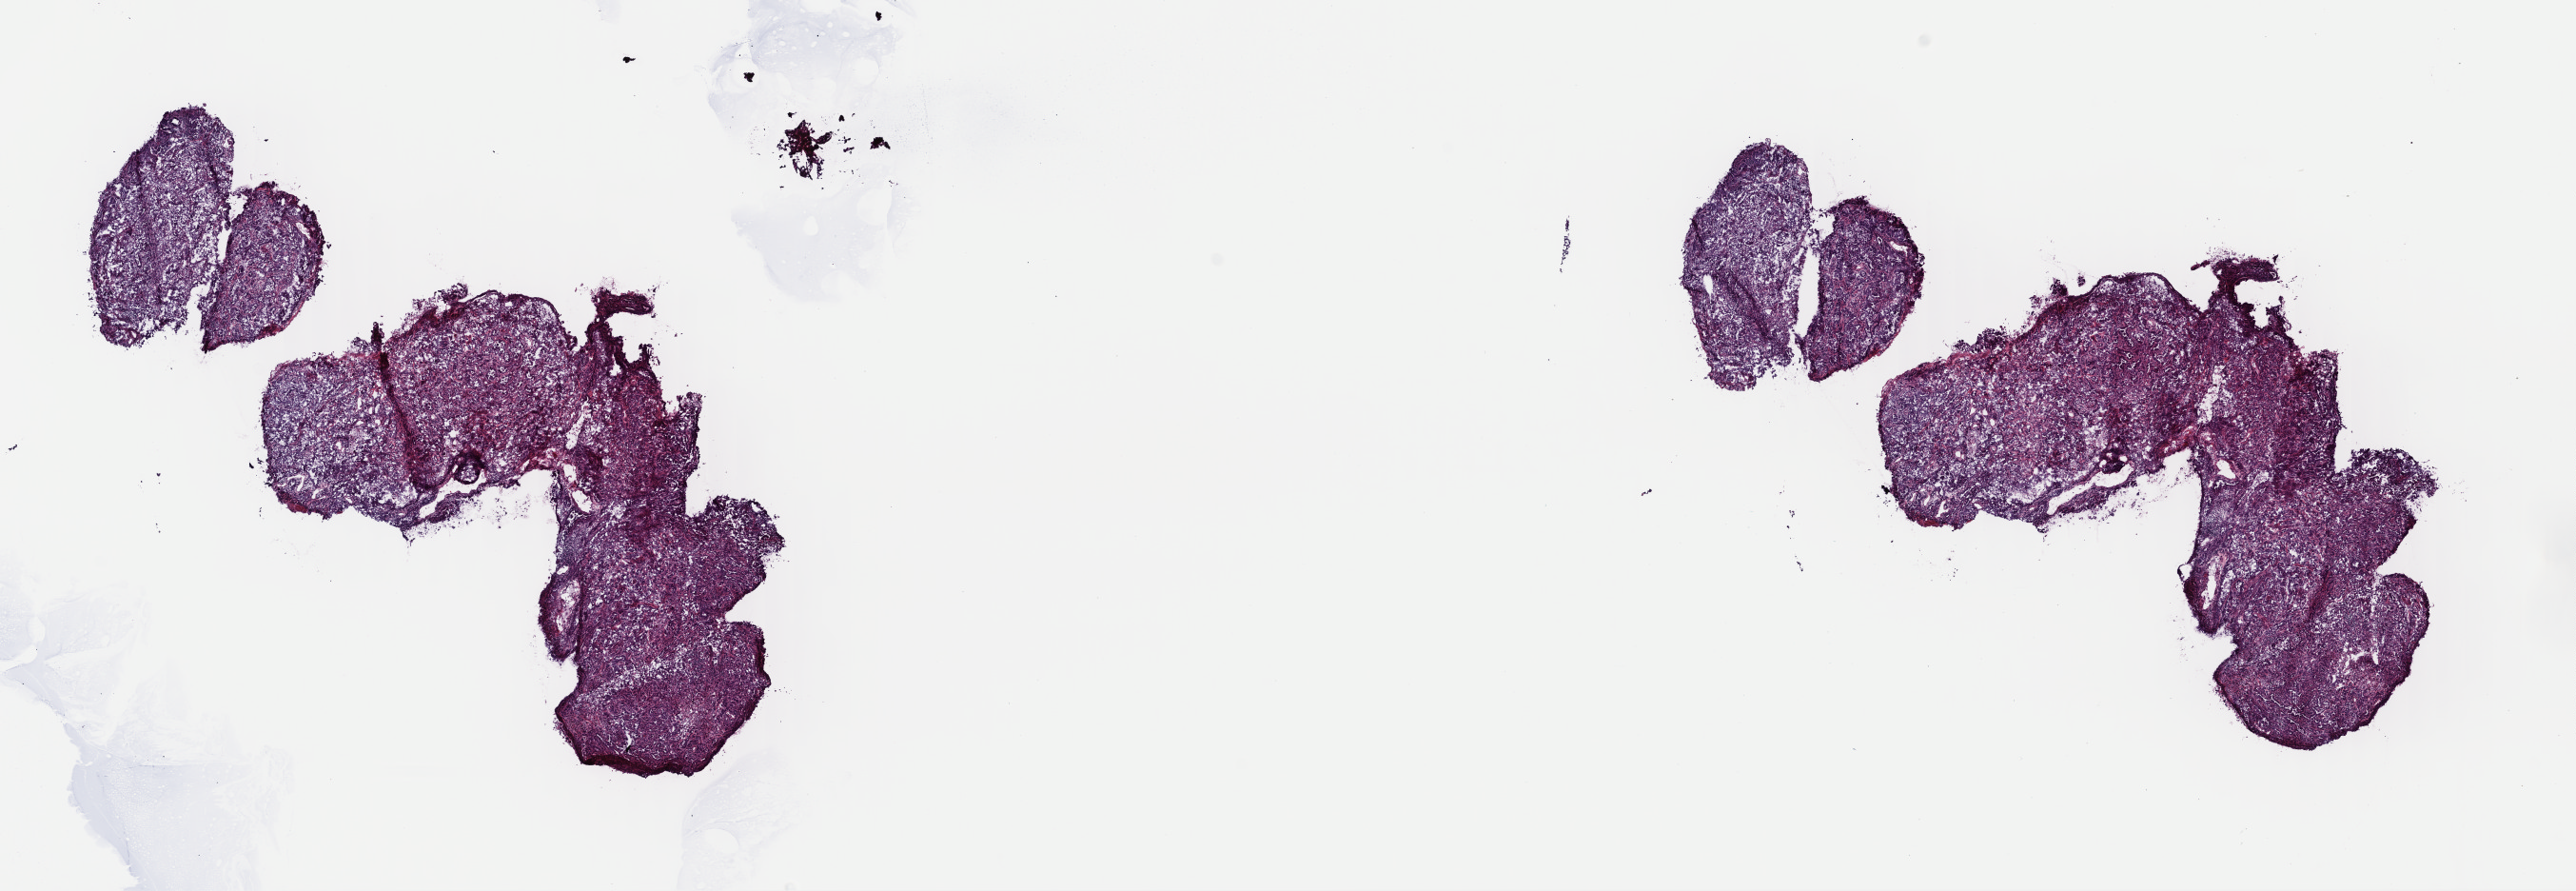
H&E whole-slide image, a low-resolution overview of the entire scanned area, about 21.3 x 7.4 mm. Frozen section from the top of the tissue portion. Sample: primary tumour, uterus. Female patient; age at initial diagnosis 56 years. Histologic grade: G3 (poorly differentiated). Pathologist review of this section (percent, as recorded): tumour cells 97%, tumour nuclei 80%, normal cells 0%, stromal cells 0%, necrosis 3%. Infiltration values recorded for this section: lymphocyte infiltration 5%, monocyte infiltration 0%, neutrophil infiltration 0%.
FIGO stage: IIIC1. Histologic diagnosis: Serous cystadenocarcinoma, NOS (endometrium).